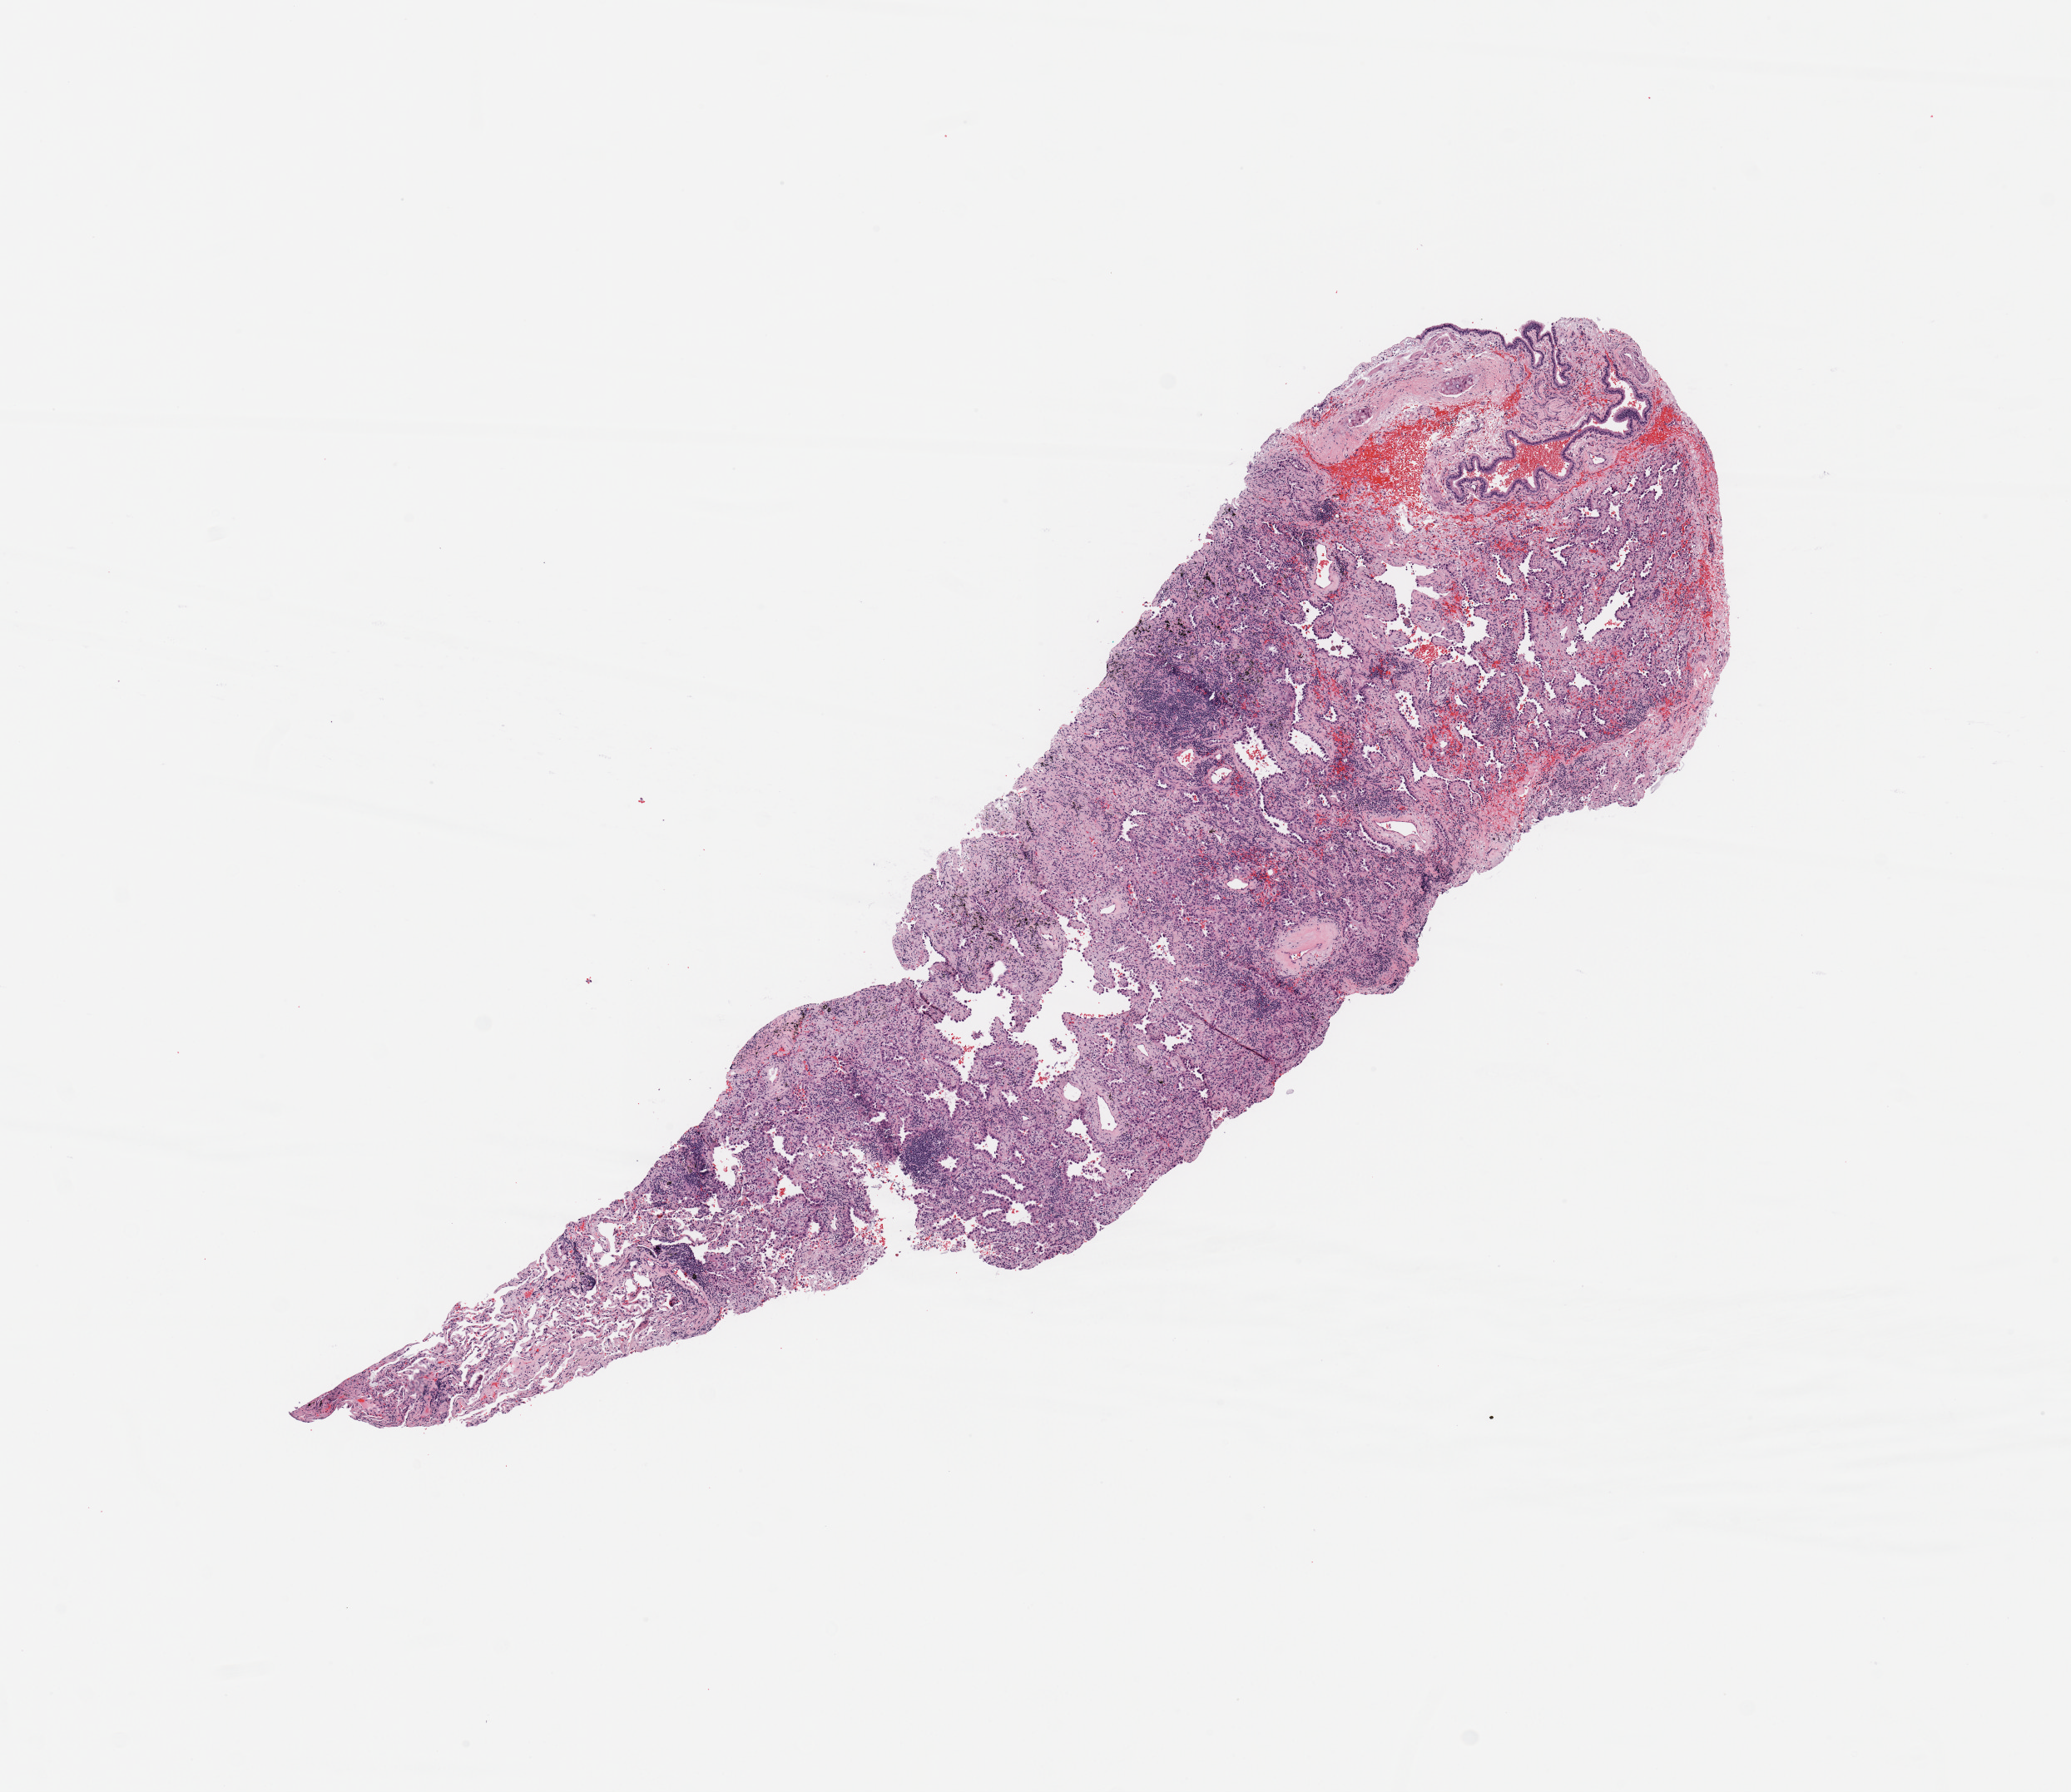
Whole-slide histology image, H&E-stained, a low-resolution overview of the entire scanned area, about 9.8 x 8.5 mm; tumour tissue sample, sampled site: lung. Female, 78 y/o. Histologic grade: G2 (moderately differentiated). Composition of this section per pathologist review: tumour nuclei 60%, necrosis 2%.
• primary tumour site (as recorded): left upper lobe
• AJCC pathologic stage: IB
• histologic diagnosis: Adenocarcinoma, NOS